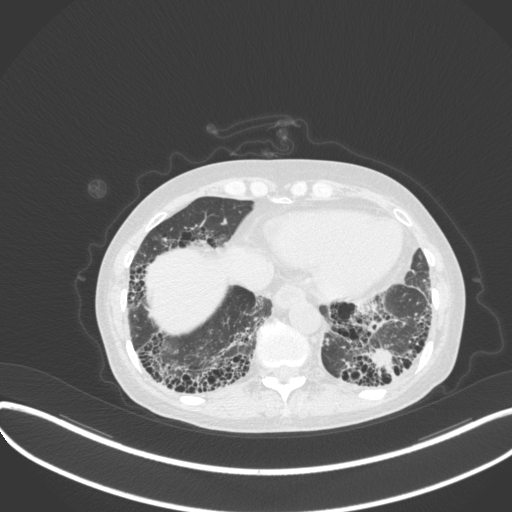
Chest CT, one axial slice. Position 68 of 373 along the scan axis. Reconstruction kernel B31f. 120 kVp. Lung window (W 1500 / L -600 HU). 512 × 512 image matrix, field of view 400 × 400 mm. Patient: female, 56 years. From the clinical record (not read from this slice): clinical TNM (as recorded): T1 N0 M0.
Structures marked on this image (bounding box drawn by a radiologist):
- lung tumour (recorded histology: adenocarcinoma): bounding box [x1, y1, x2, y2] px = [366, 346, 401, 379]